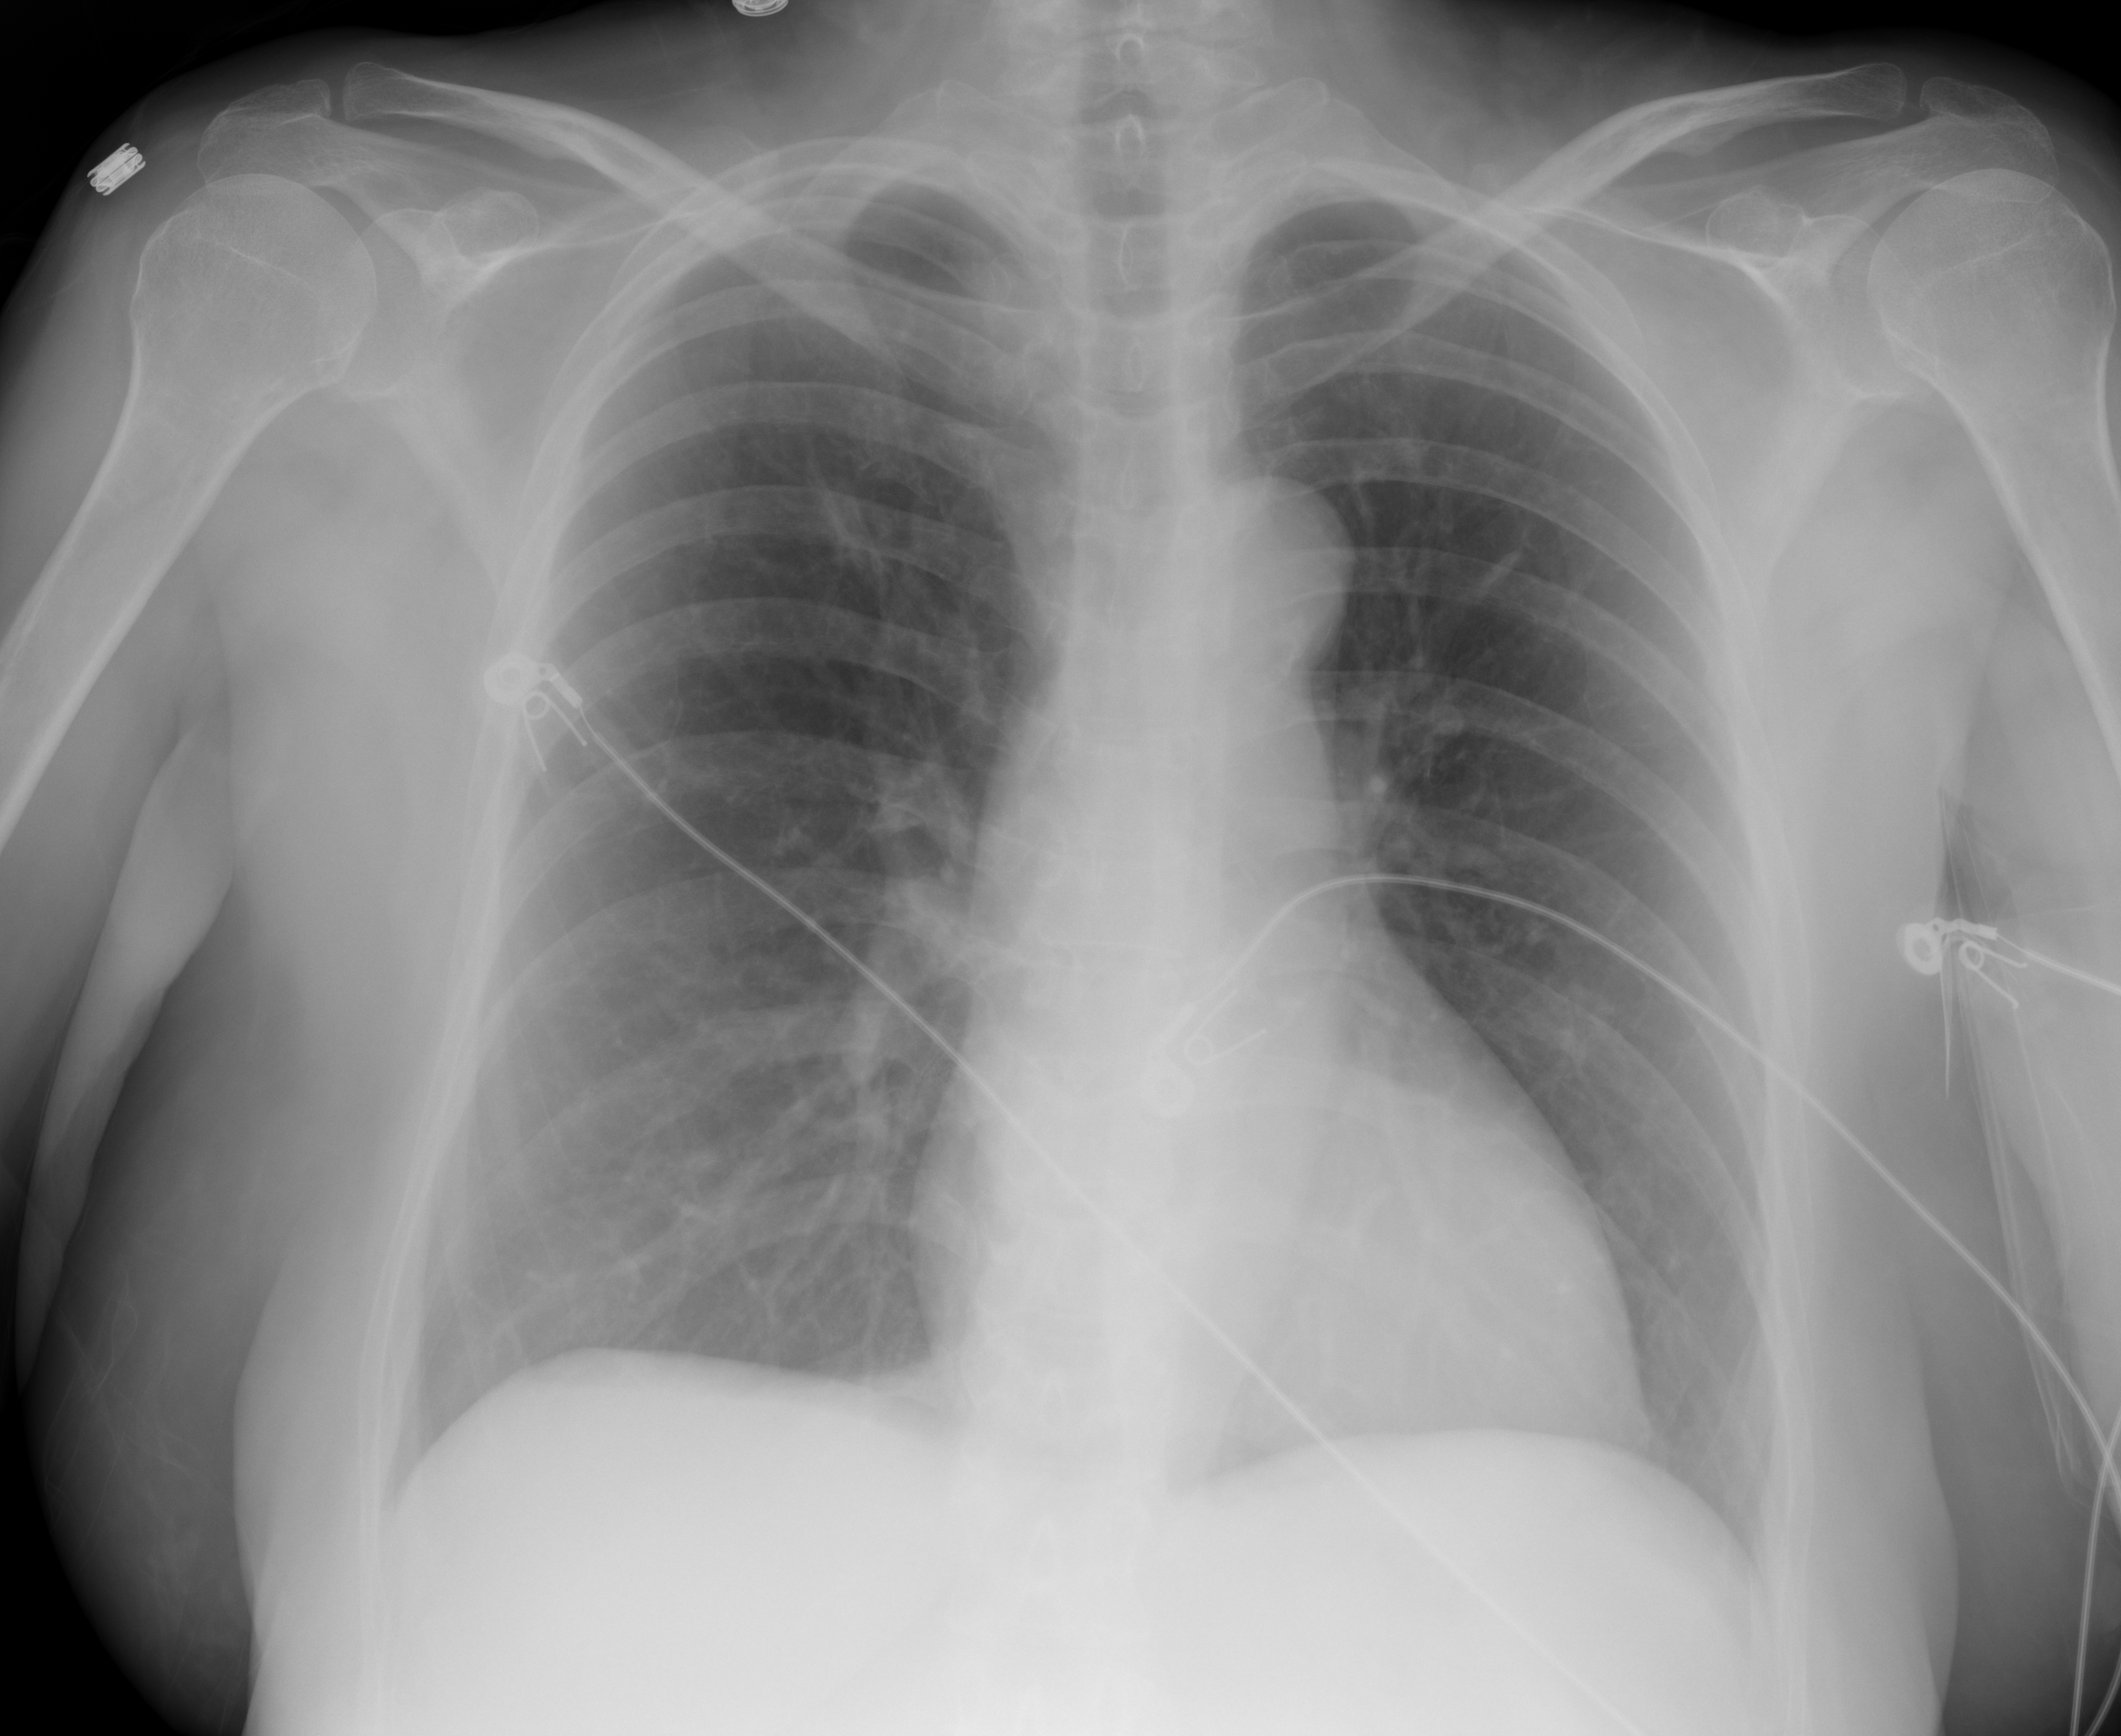
Portable chest radiograph, AP projection. Female patient, age 59 years; COVID-19 (test-positive).
Key findings recorded by the radiologist: he lungs are clear and without acute airspace disease.